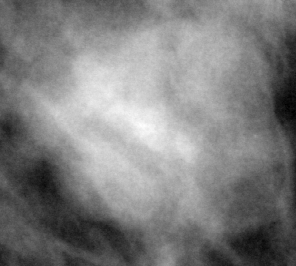
Cropped region of a digitized screen-film mammogram centred on a radiologist-marked abnormality; left breast; MLO view.
Finding: mass, shape lobulated, margins circumscribed; BI-RADS assessment category 4; pathology result (as recorded, not read from the image): benign.